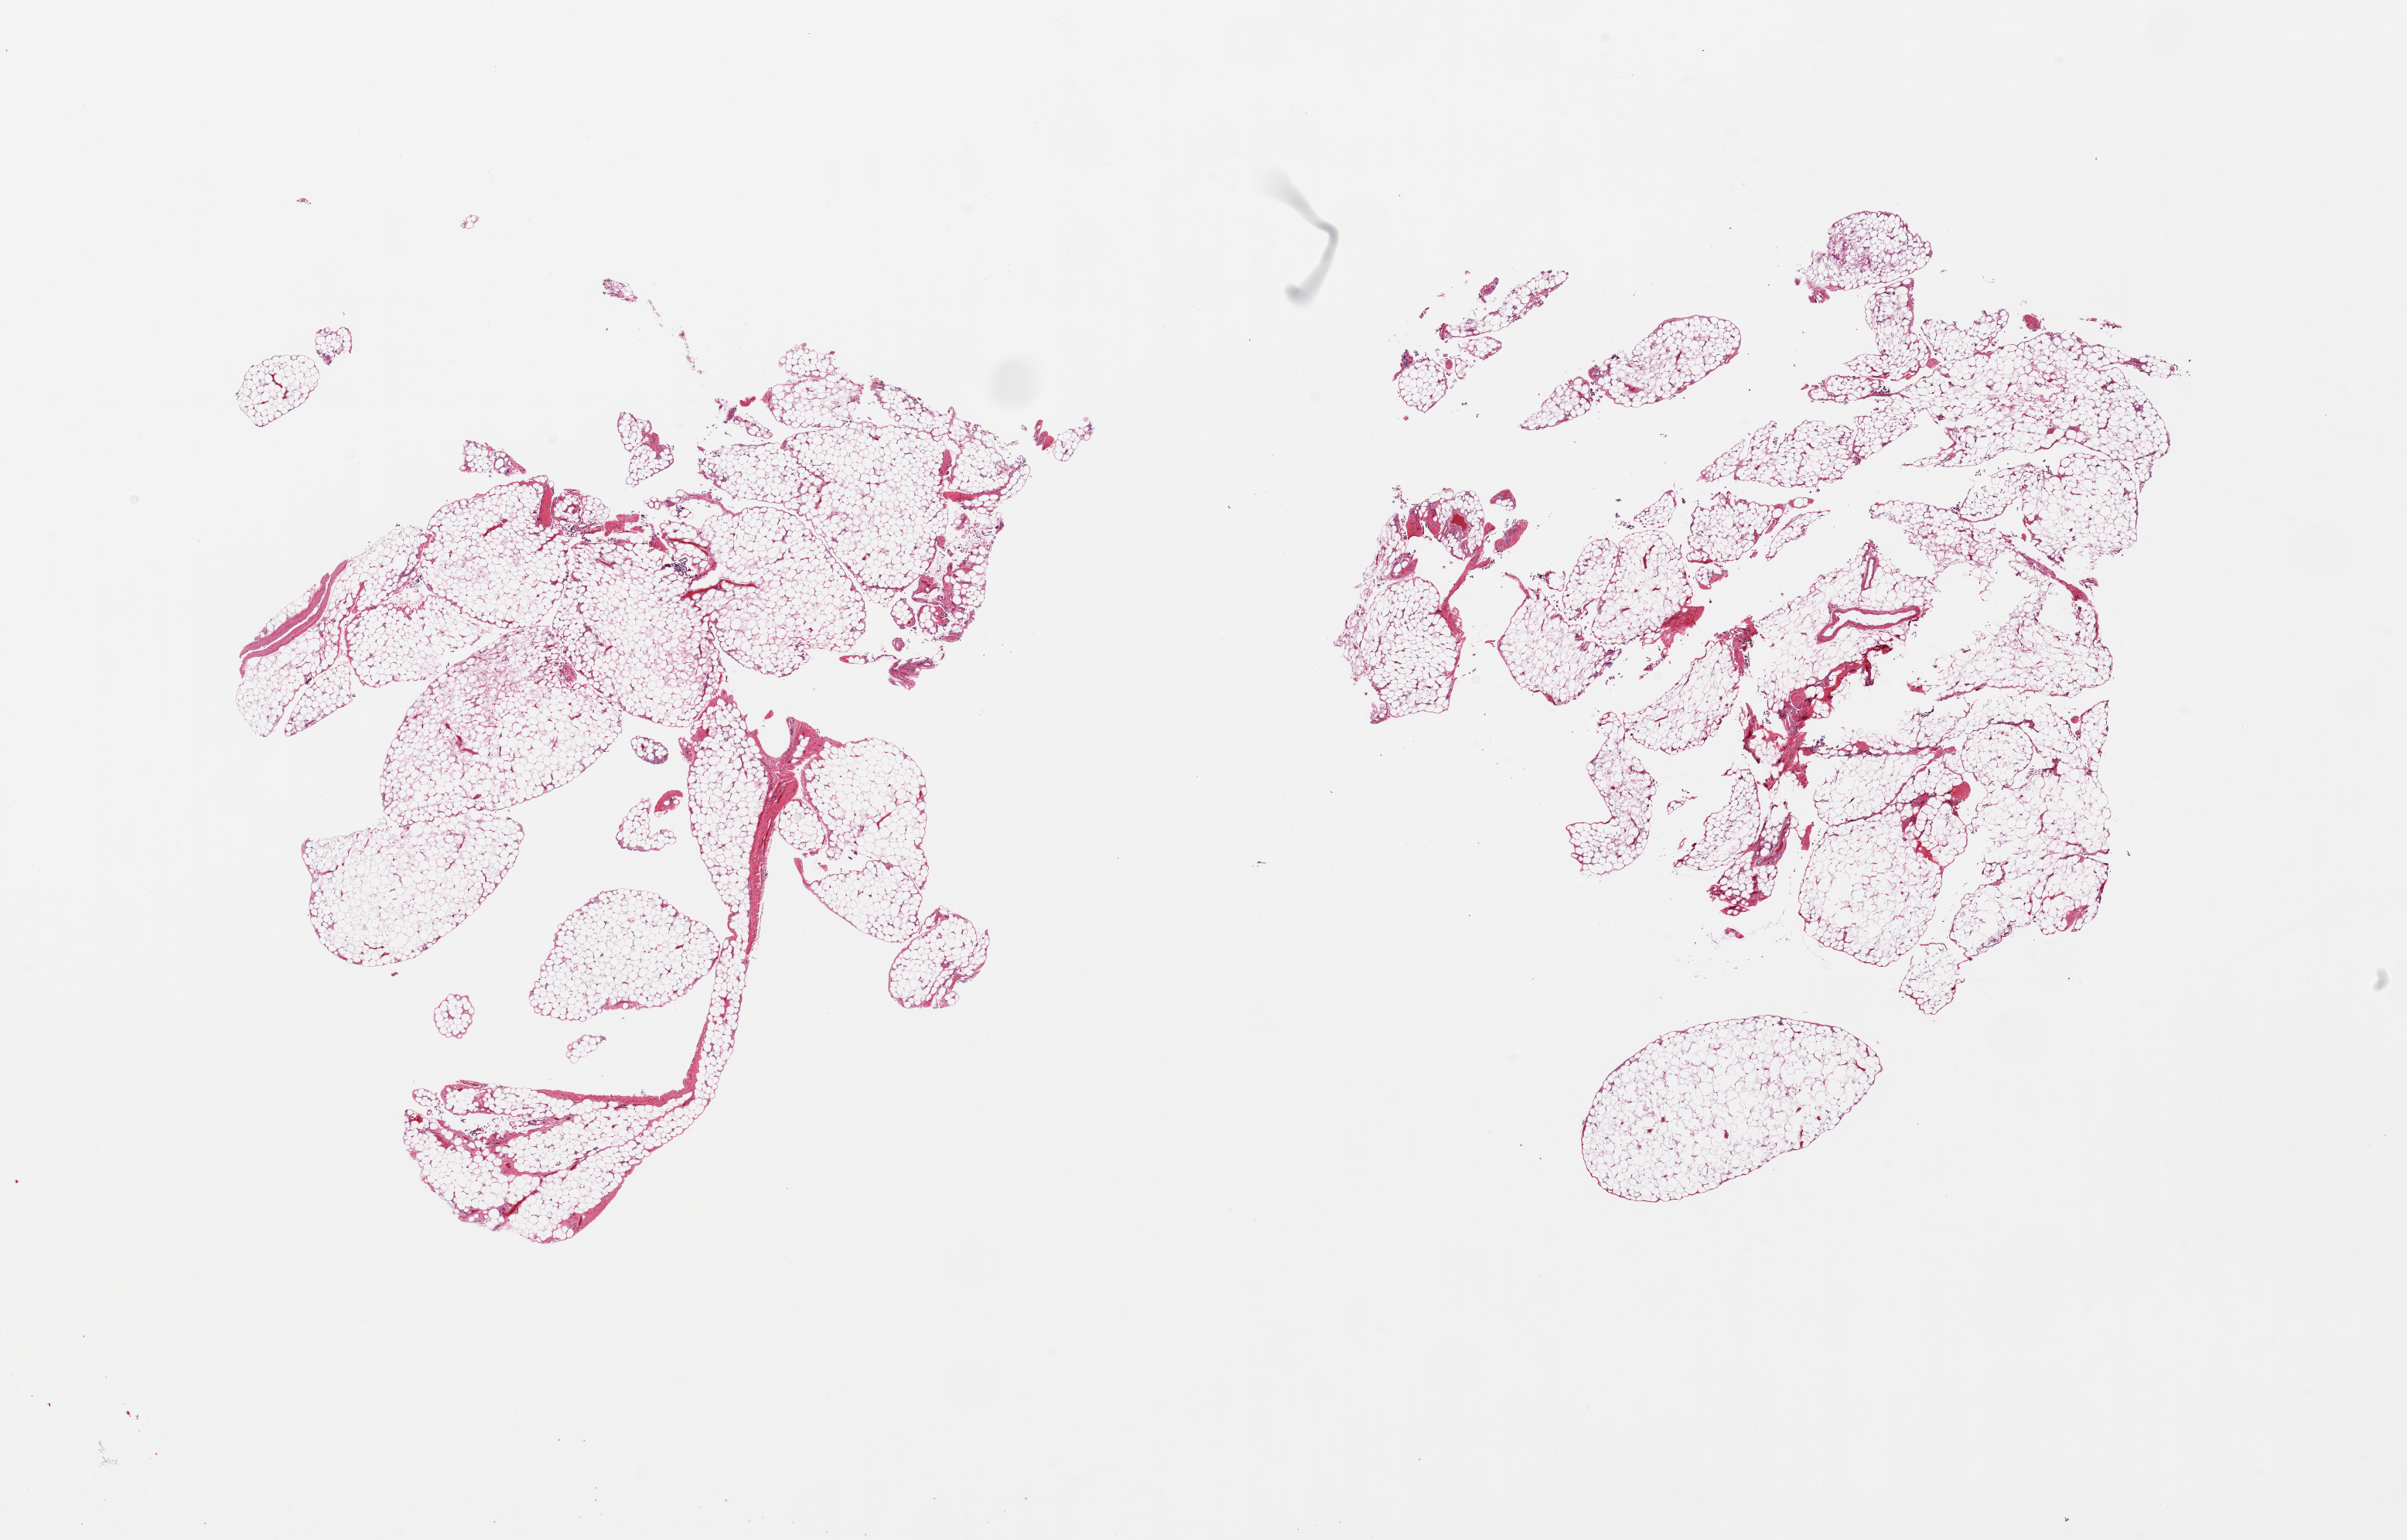
Whole-slide image, H&E stain, brightfield — whole scanned area (about 24.6 x 15.7 mm, acquisition: 20x scan) shown as a low-resolution overview, PAXgene-fixed, paraffin-embedded tissue, section of omentum (target tissue), tissue donor sample. Male donor.
Review note (as recorded): 2 pieces; <5% fibrous content.